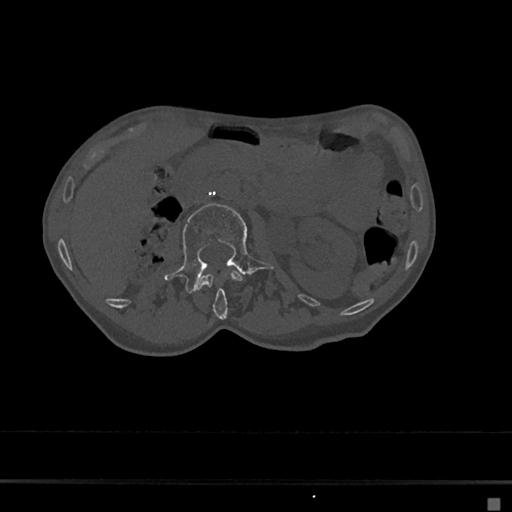
CT including the spine, one axial slice. Reconstruction kernel Br40s/3. Bone window (W 1800 / L 400 HU). 0.5 mm slice thickness. 512 × 512 image matrix. Female patient, age 68 years. From the clinical record (not read from this slice): primary cancer: renal.
Structures marked on this image (semi-automatically segmented with operator editing):
- L1 vertebra: bounding box [x1, y1, x2, y2] px = [196, 270, 242, 319]
- L2 vertebra: [164, 203, 274, 293]